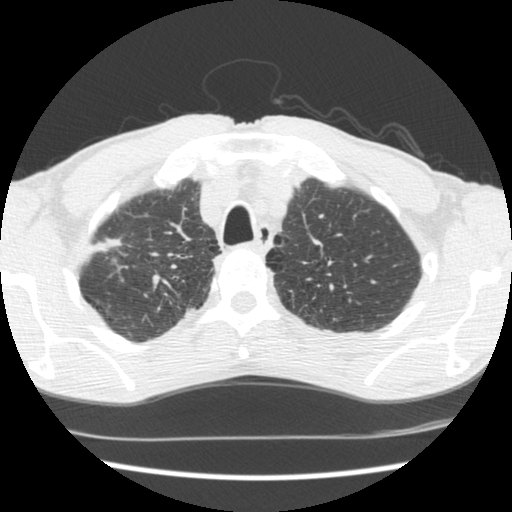
Low-dose screening chest CT, axial slice; baseline screening round; lung window (W 1500 / L -600 HU); 2.5 mm slice thickness; 120 kVp; 512 × 512 image matrix. Male participant, aged 62 years at enrolment.
Expert reader's lesion annotation, bounding box (x1, y1, x2, y2) in pixels: (79, 220, 133, 274). Screening reader's record for this exam: no non-calcified nodule ≥4 mm recorded. Lung cancer was diagnosed 640 days after this screen: adenocarcinoma, NOS, right upper lobe, poorly differentiated (G3), stage IIA (AJCC 6th edition), 22 mm at pathology.